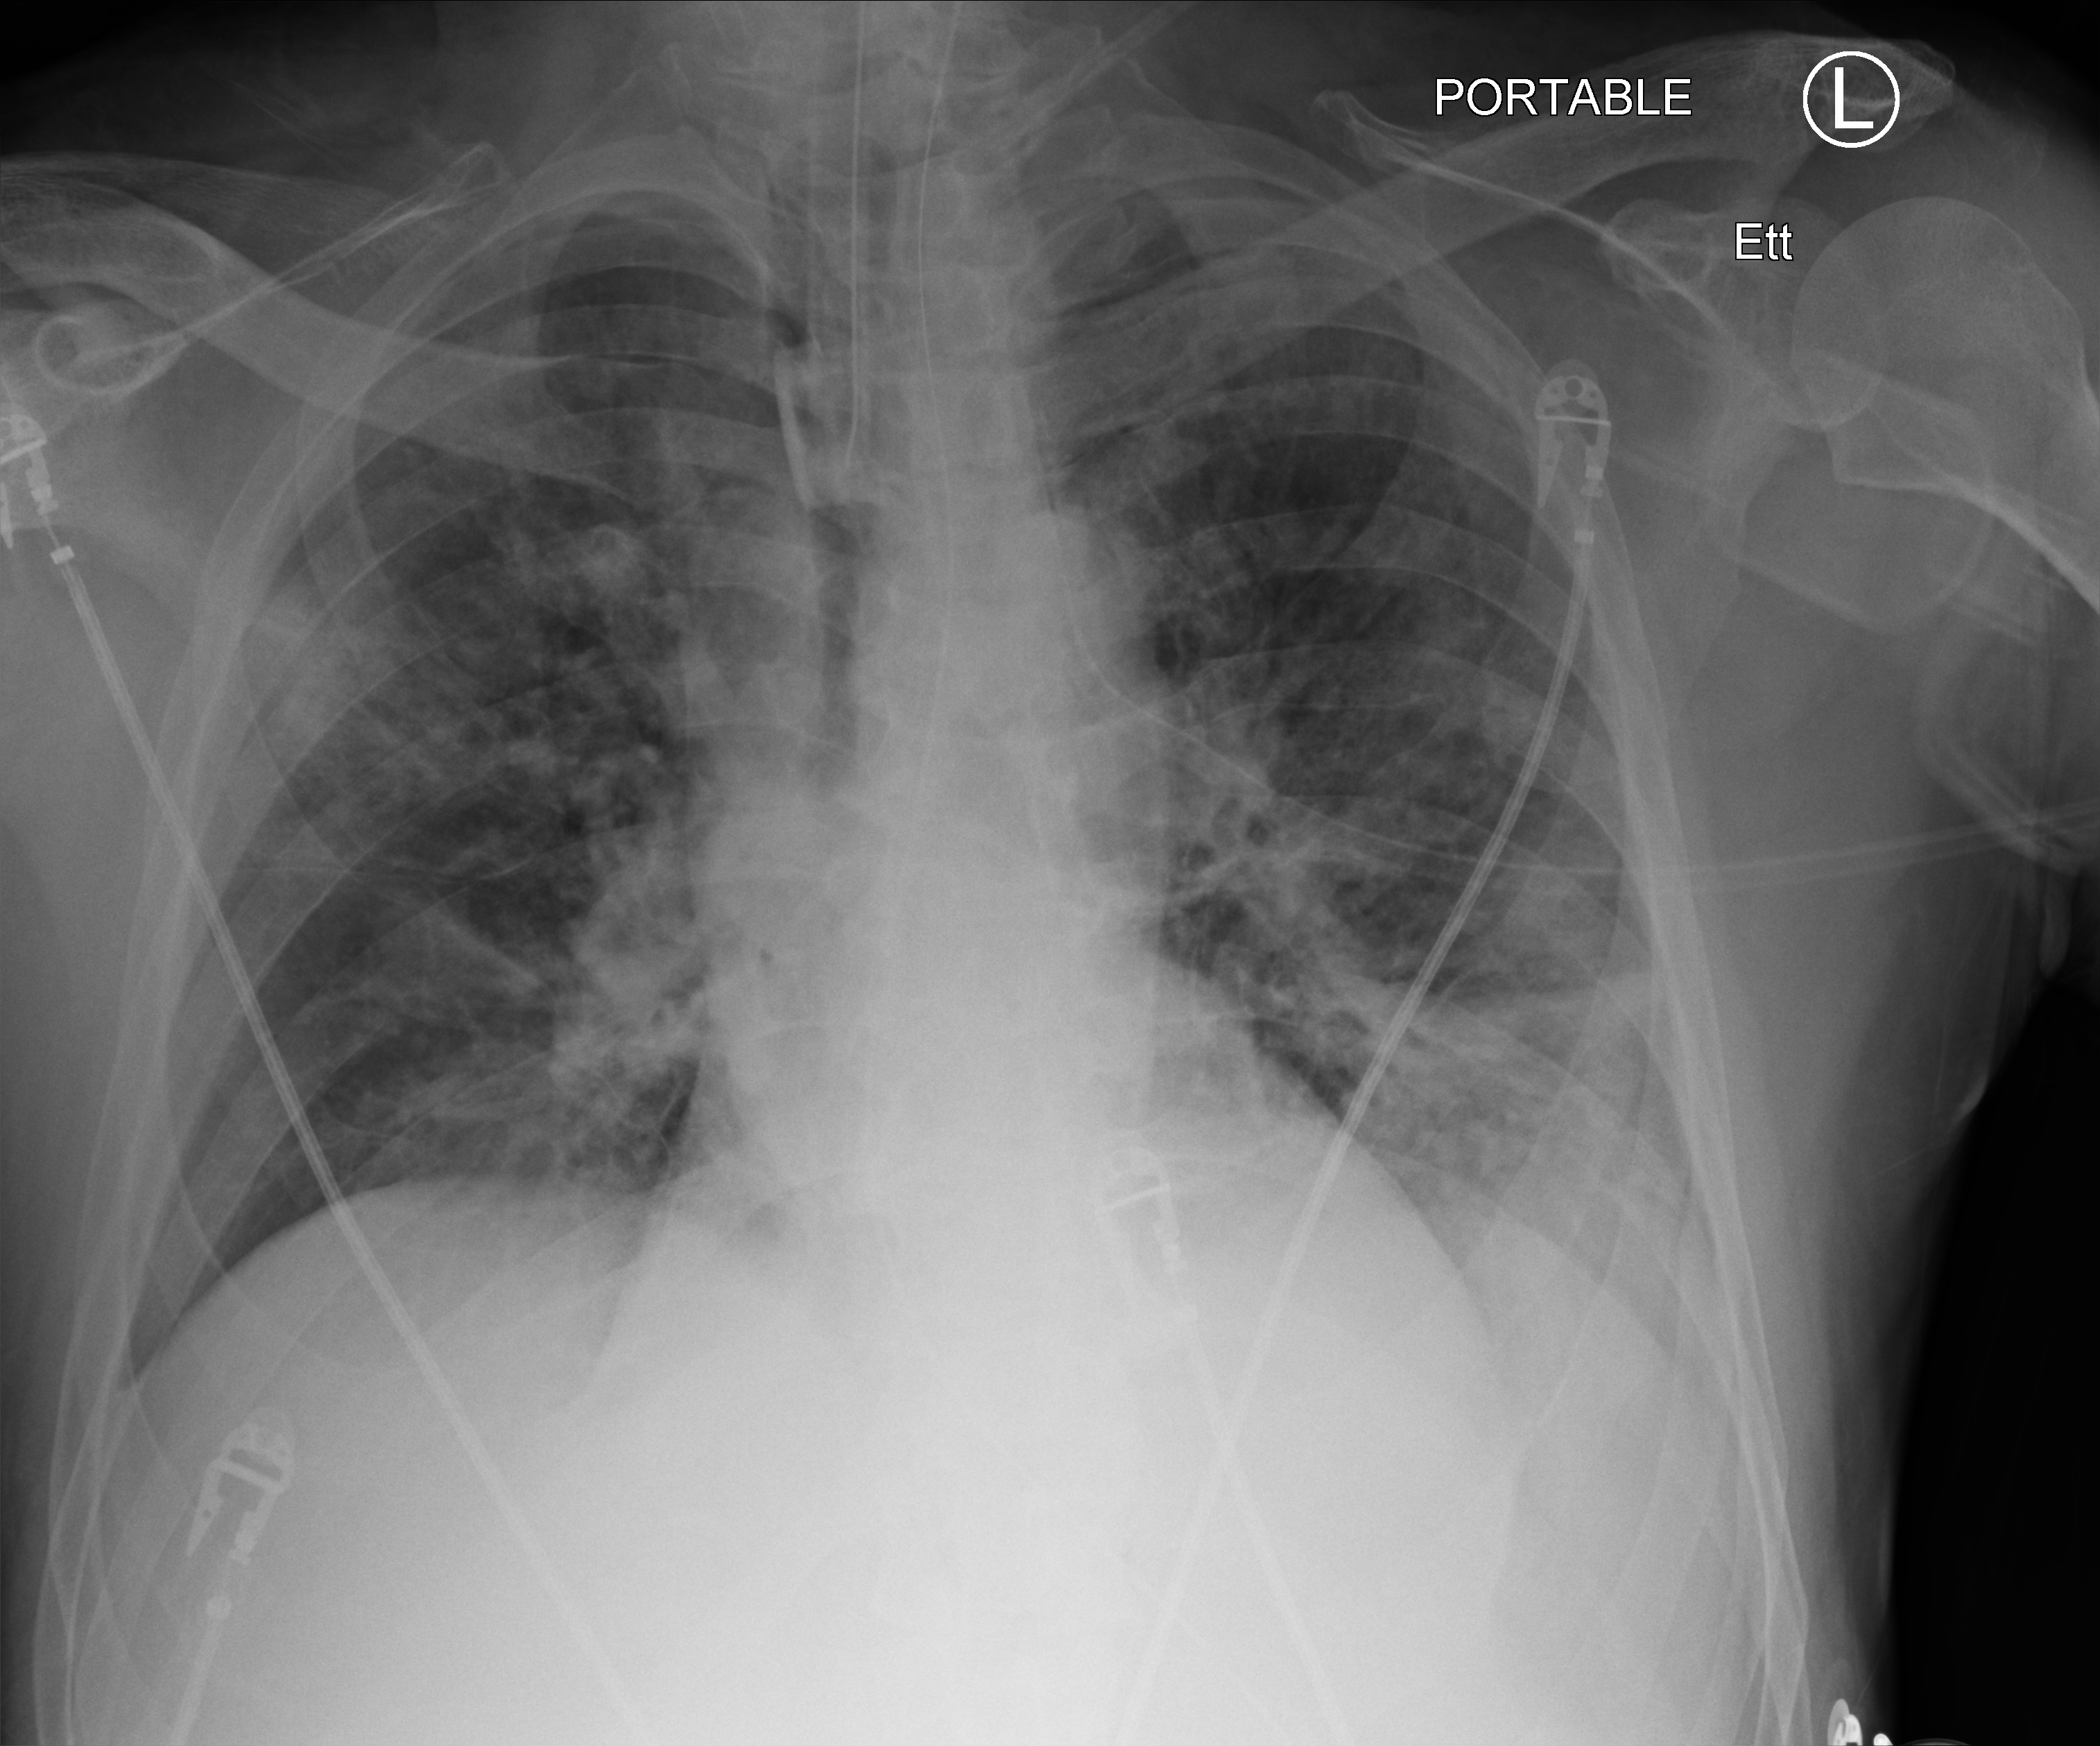
Portable chest radiograph; anteroposterior (AP) projection. Patient hospitalised with COVID-19; male, aged 60–74 years.
Admission-level facts for this patient (not findings on this image; timing relative to this image not recorded): smoking status (admission record): never; diabetes (admission record): yes.